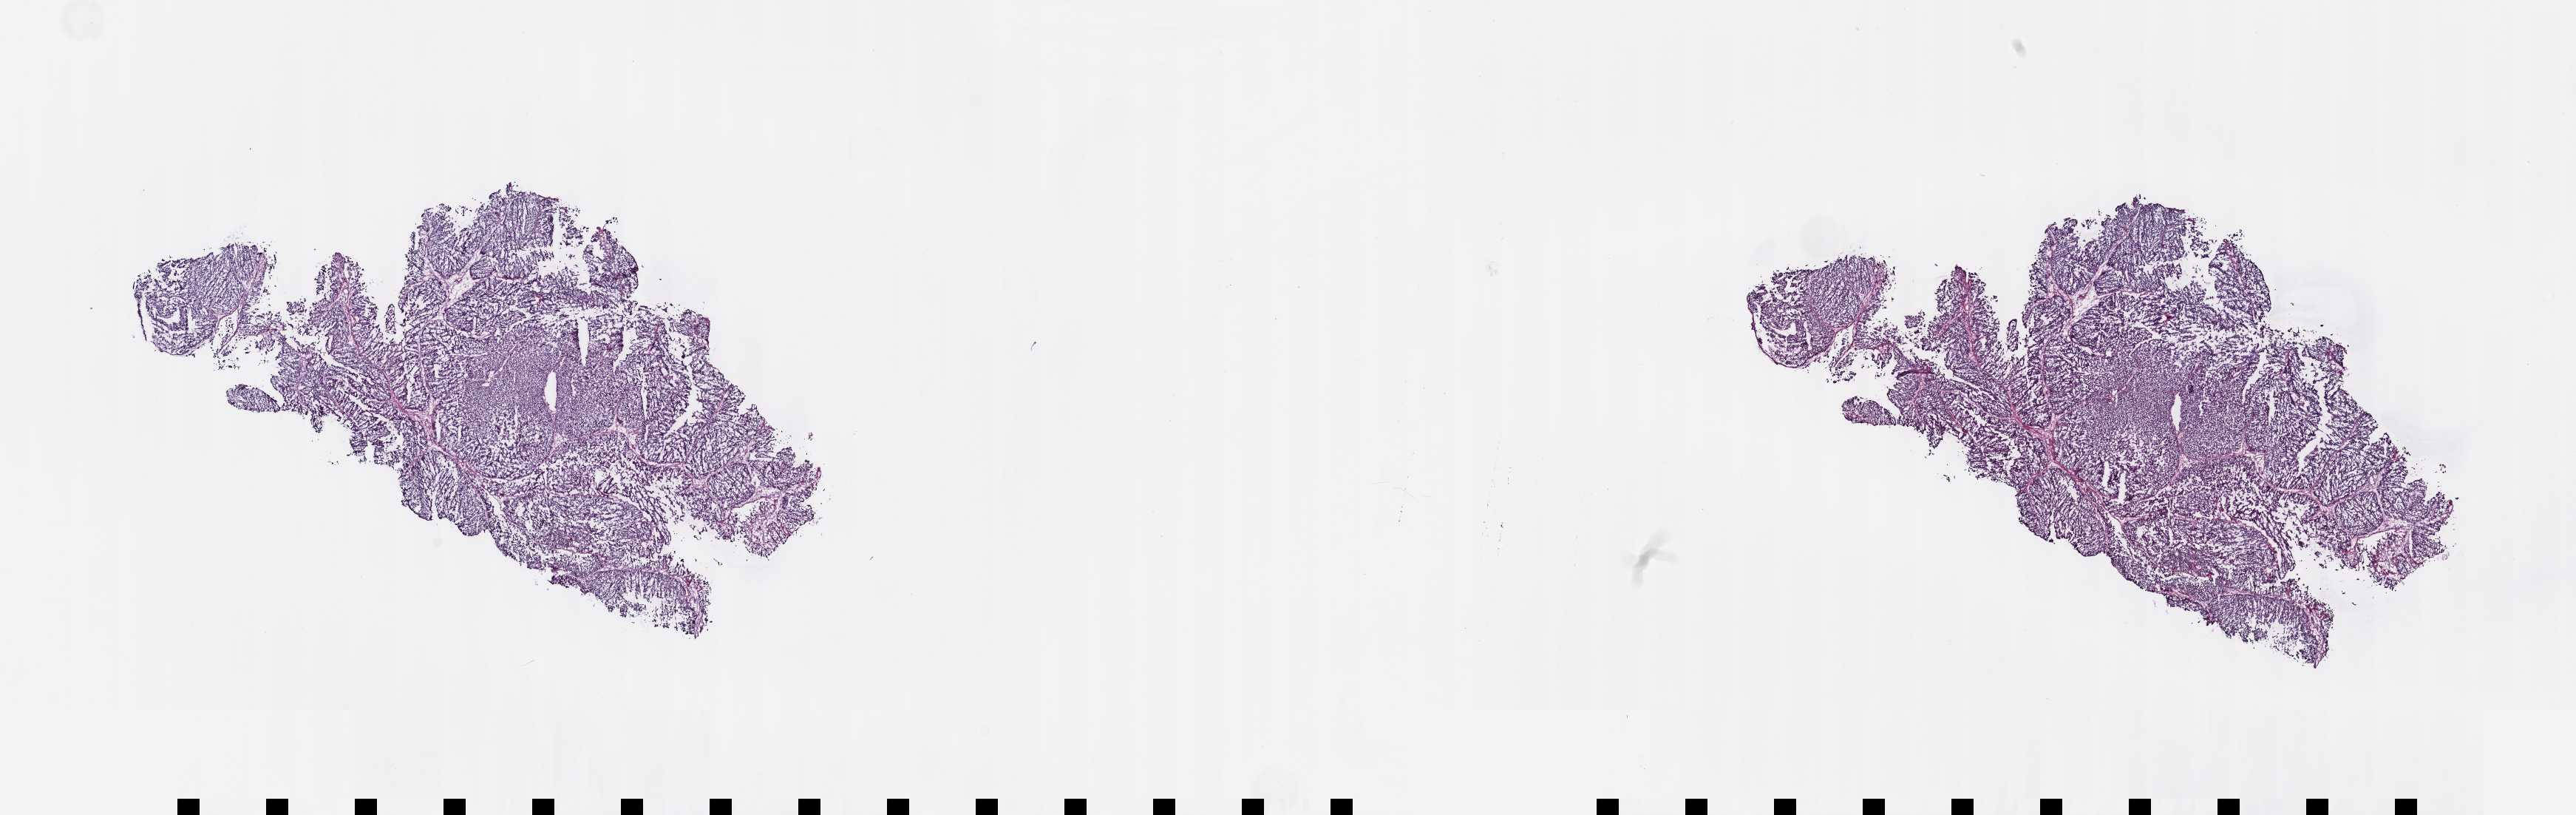
H&E whole-slide image, low-resolution overview of the scanned area, about 28.2 x 8.9 mm (acquisition: 40x scan). Frozen section from the top of the tissue portion. Primary tumour sample from the bladder. Patient: male, age at initial diagnosis 79 years. Histologic grade: high grade. Pathologist review of this section (percent, as recorded): tumour cells 100%, tumour nuclei 80%, normal cells 0%, stromal cells 0%, necrosis 0%. Infiltration values recorded for this section: lymphocyte infiltration 2%, monocyte infiltration 0%, neutrophil infiltration 0%.
Lymph nodes positive (case pathology): 97 of 140 examined. Pathologic diagnosis: Papillary transitional cell carcinoma. AJCC pathologic stage: IV (6th edition).